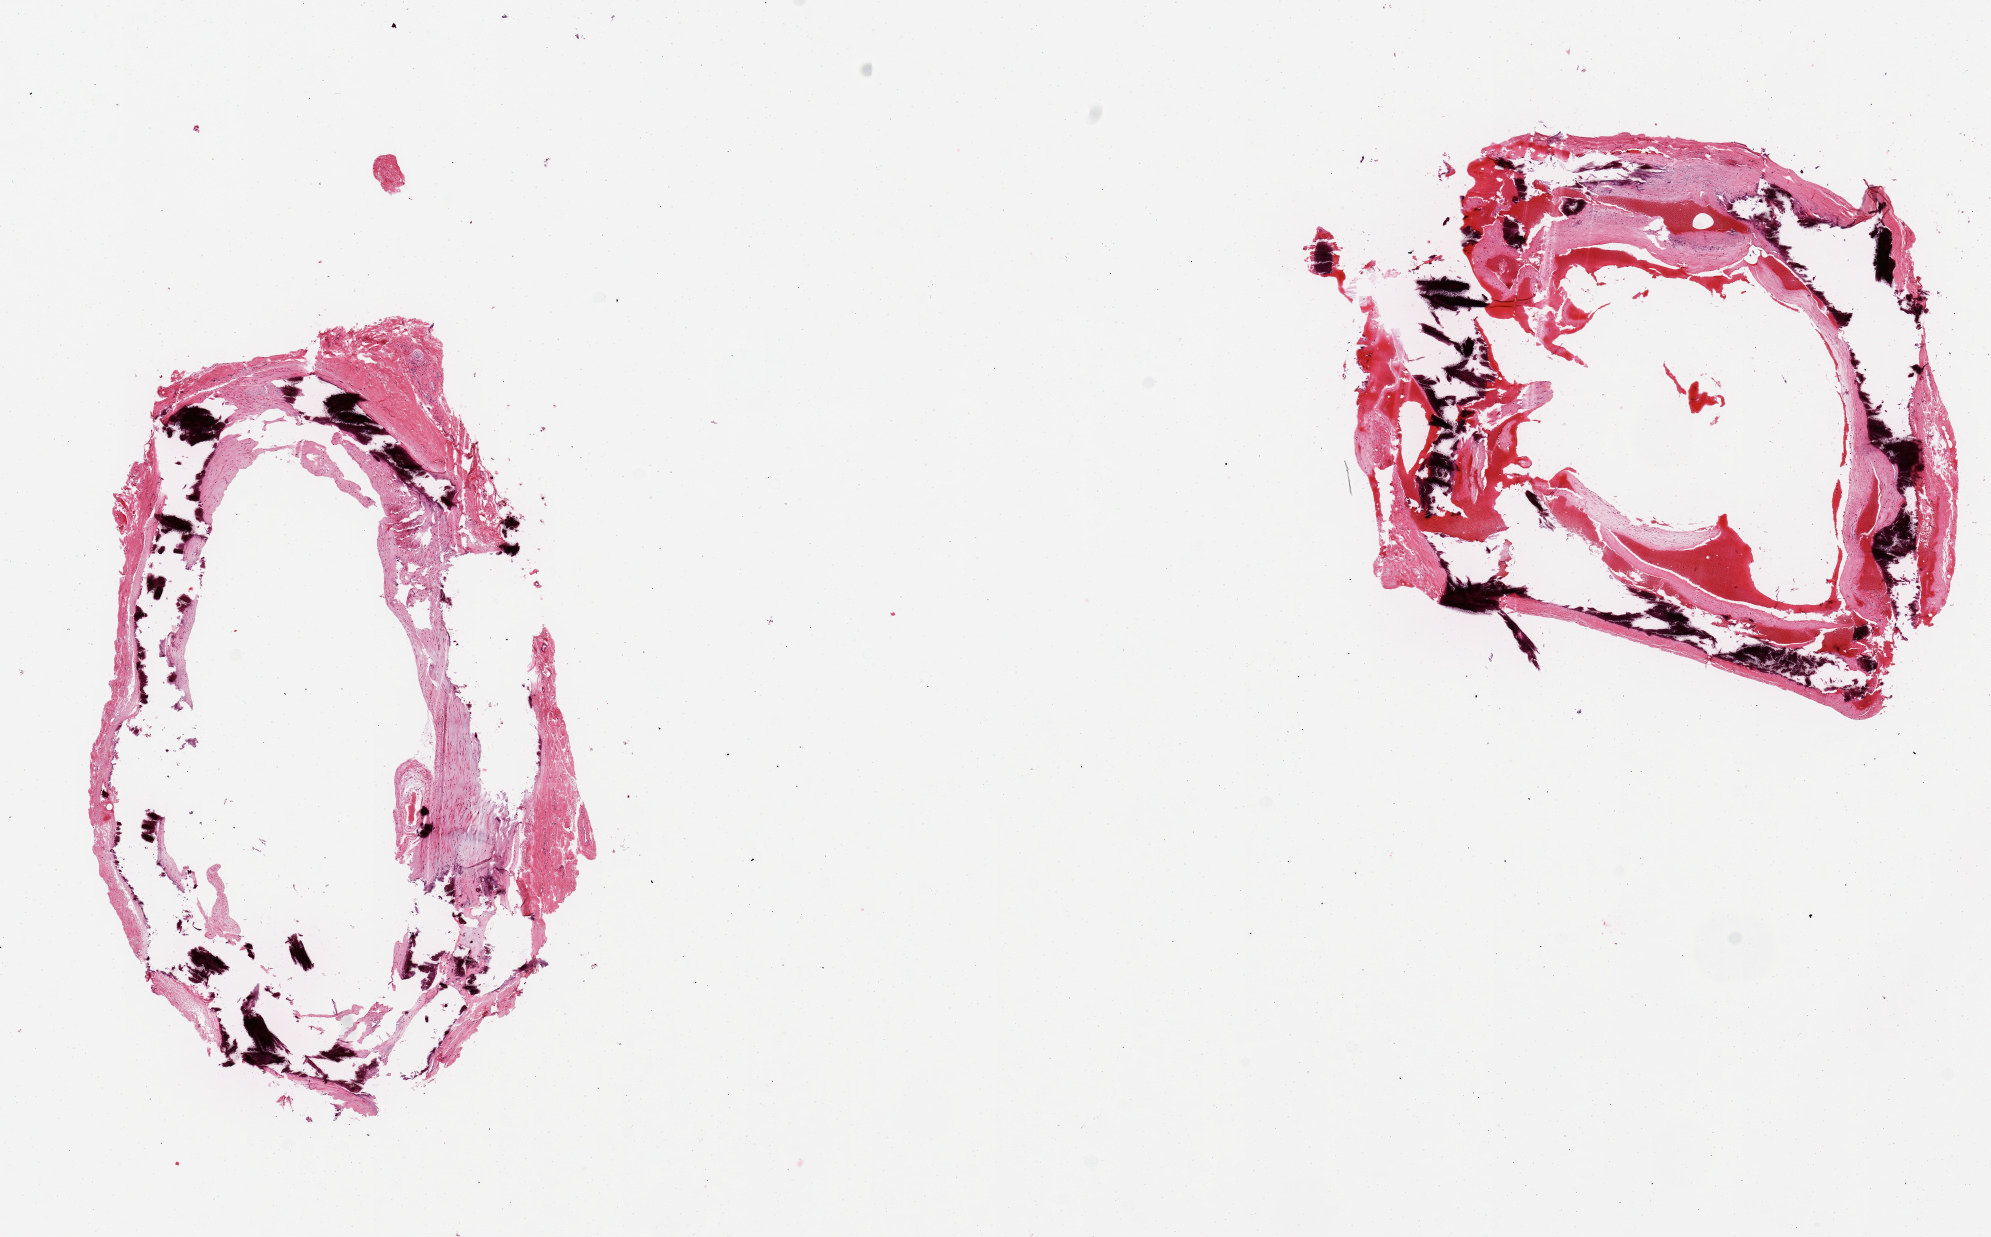
Whole-slide image, haematoxylin and eosin stain, brightfield, a low-resolution overview of the entire scanned area, about 15.8 x 9.8 mm; PAXgene-fixed paraffin-embedded (PFPE) section; section of tibial artery (target tissue); tissue donor sample.
• pathologist's review note for this sample: 2 pieces; fragmented secondary to severe calcification, atherosclerosis